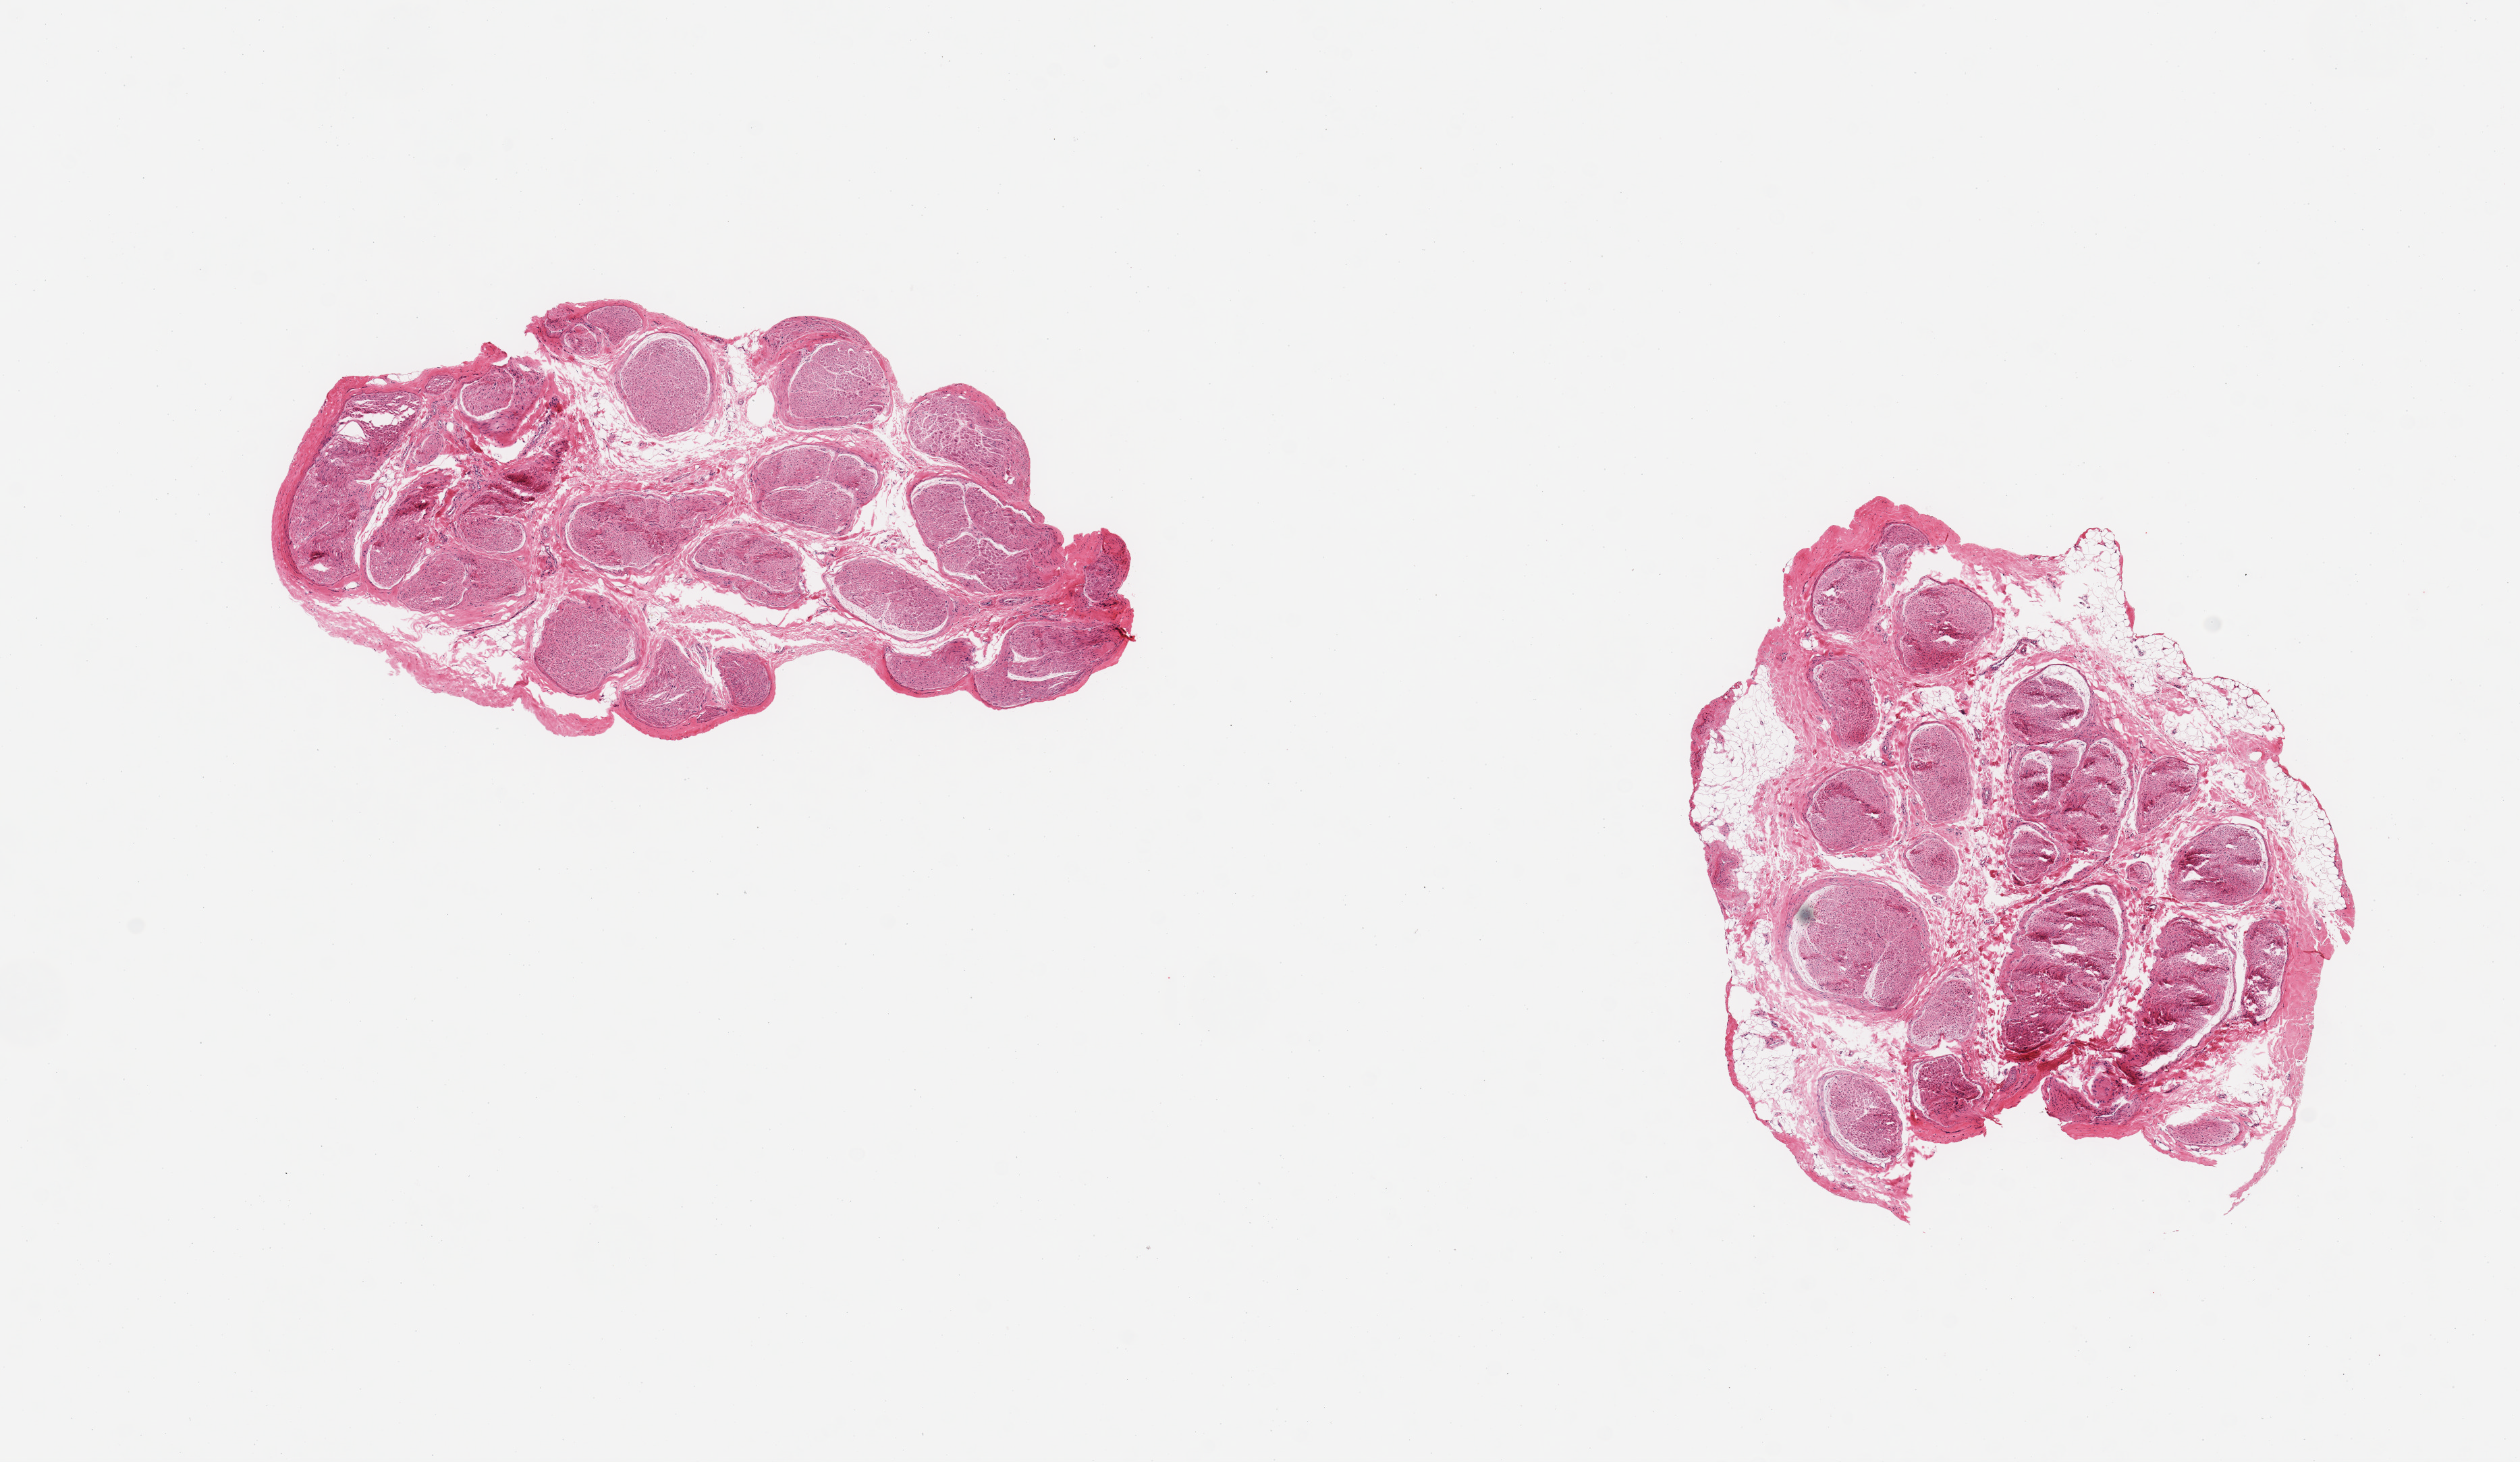
Digitized hematoxylin and eosin (H&E)-stained section, brightfield, whole scanned area (about 14.8 x 8.6 mm, acquisition: 20x scan) shown as a low-resolution overview; PAXgene-fixed, paraffin-embedded tissue; target tissue: tibial nerve; donor tissue sample. Donor sex: female.
Reviewer comment on this tissue sample: 2 pieces; 20% internal fat.